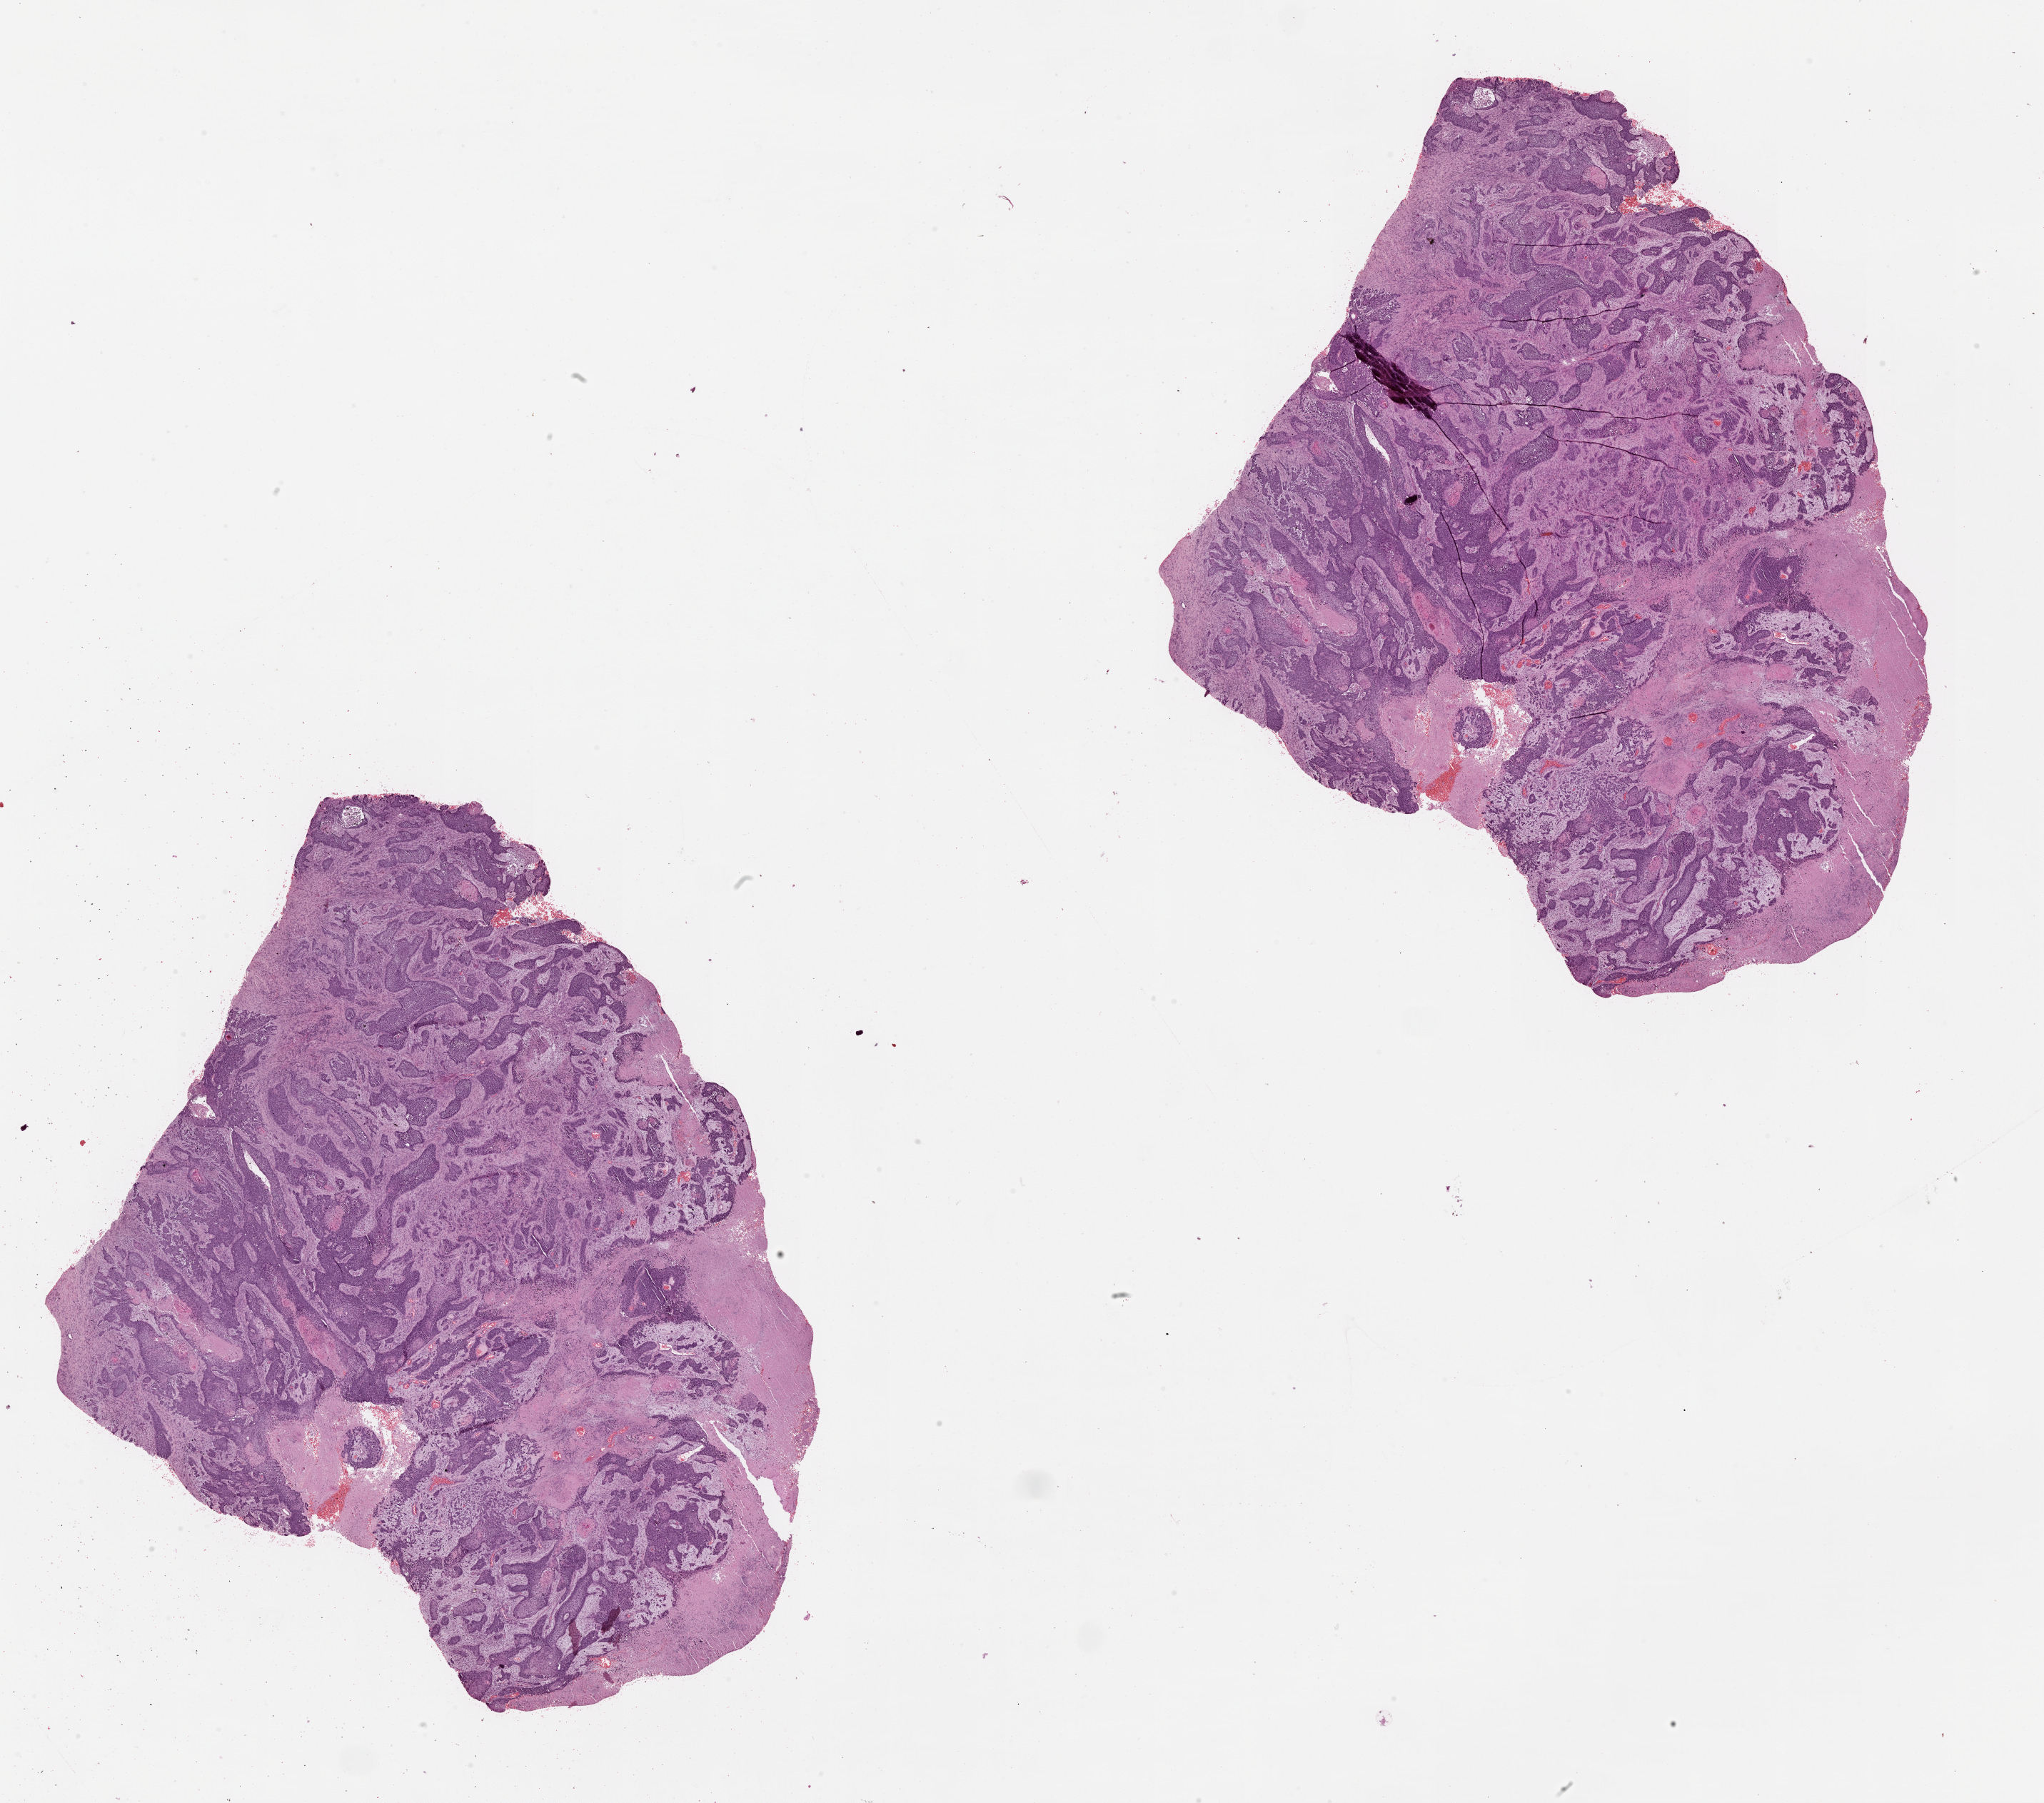
H&E whole-slide image, shown as a low-resolution overview of the whole scanned area (about 23.1 x 20.3 mm). Lung, tumour tissue. Patient: male, age 59 years.
Patient diagnosis (cohort enrolment): squamous cell carcinoma (lung).